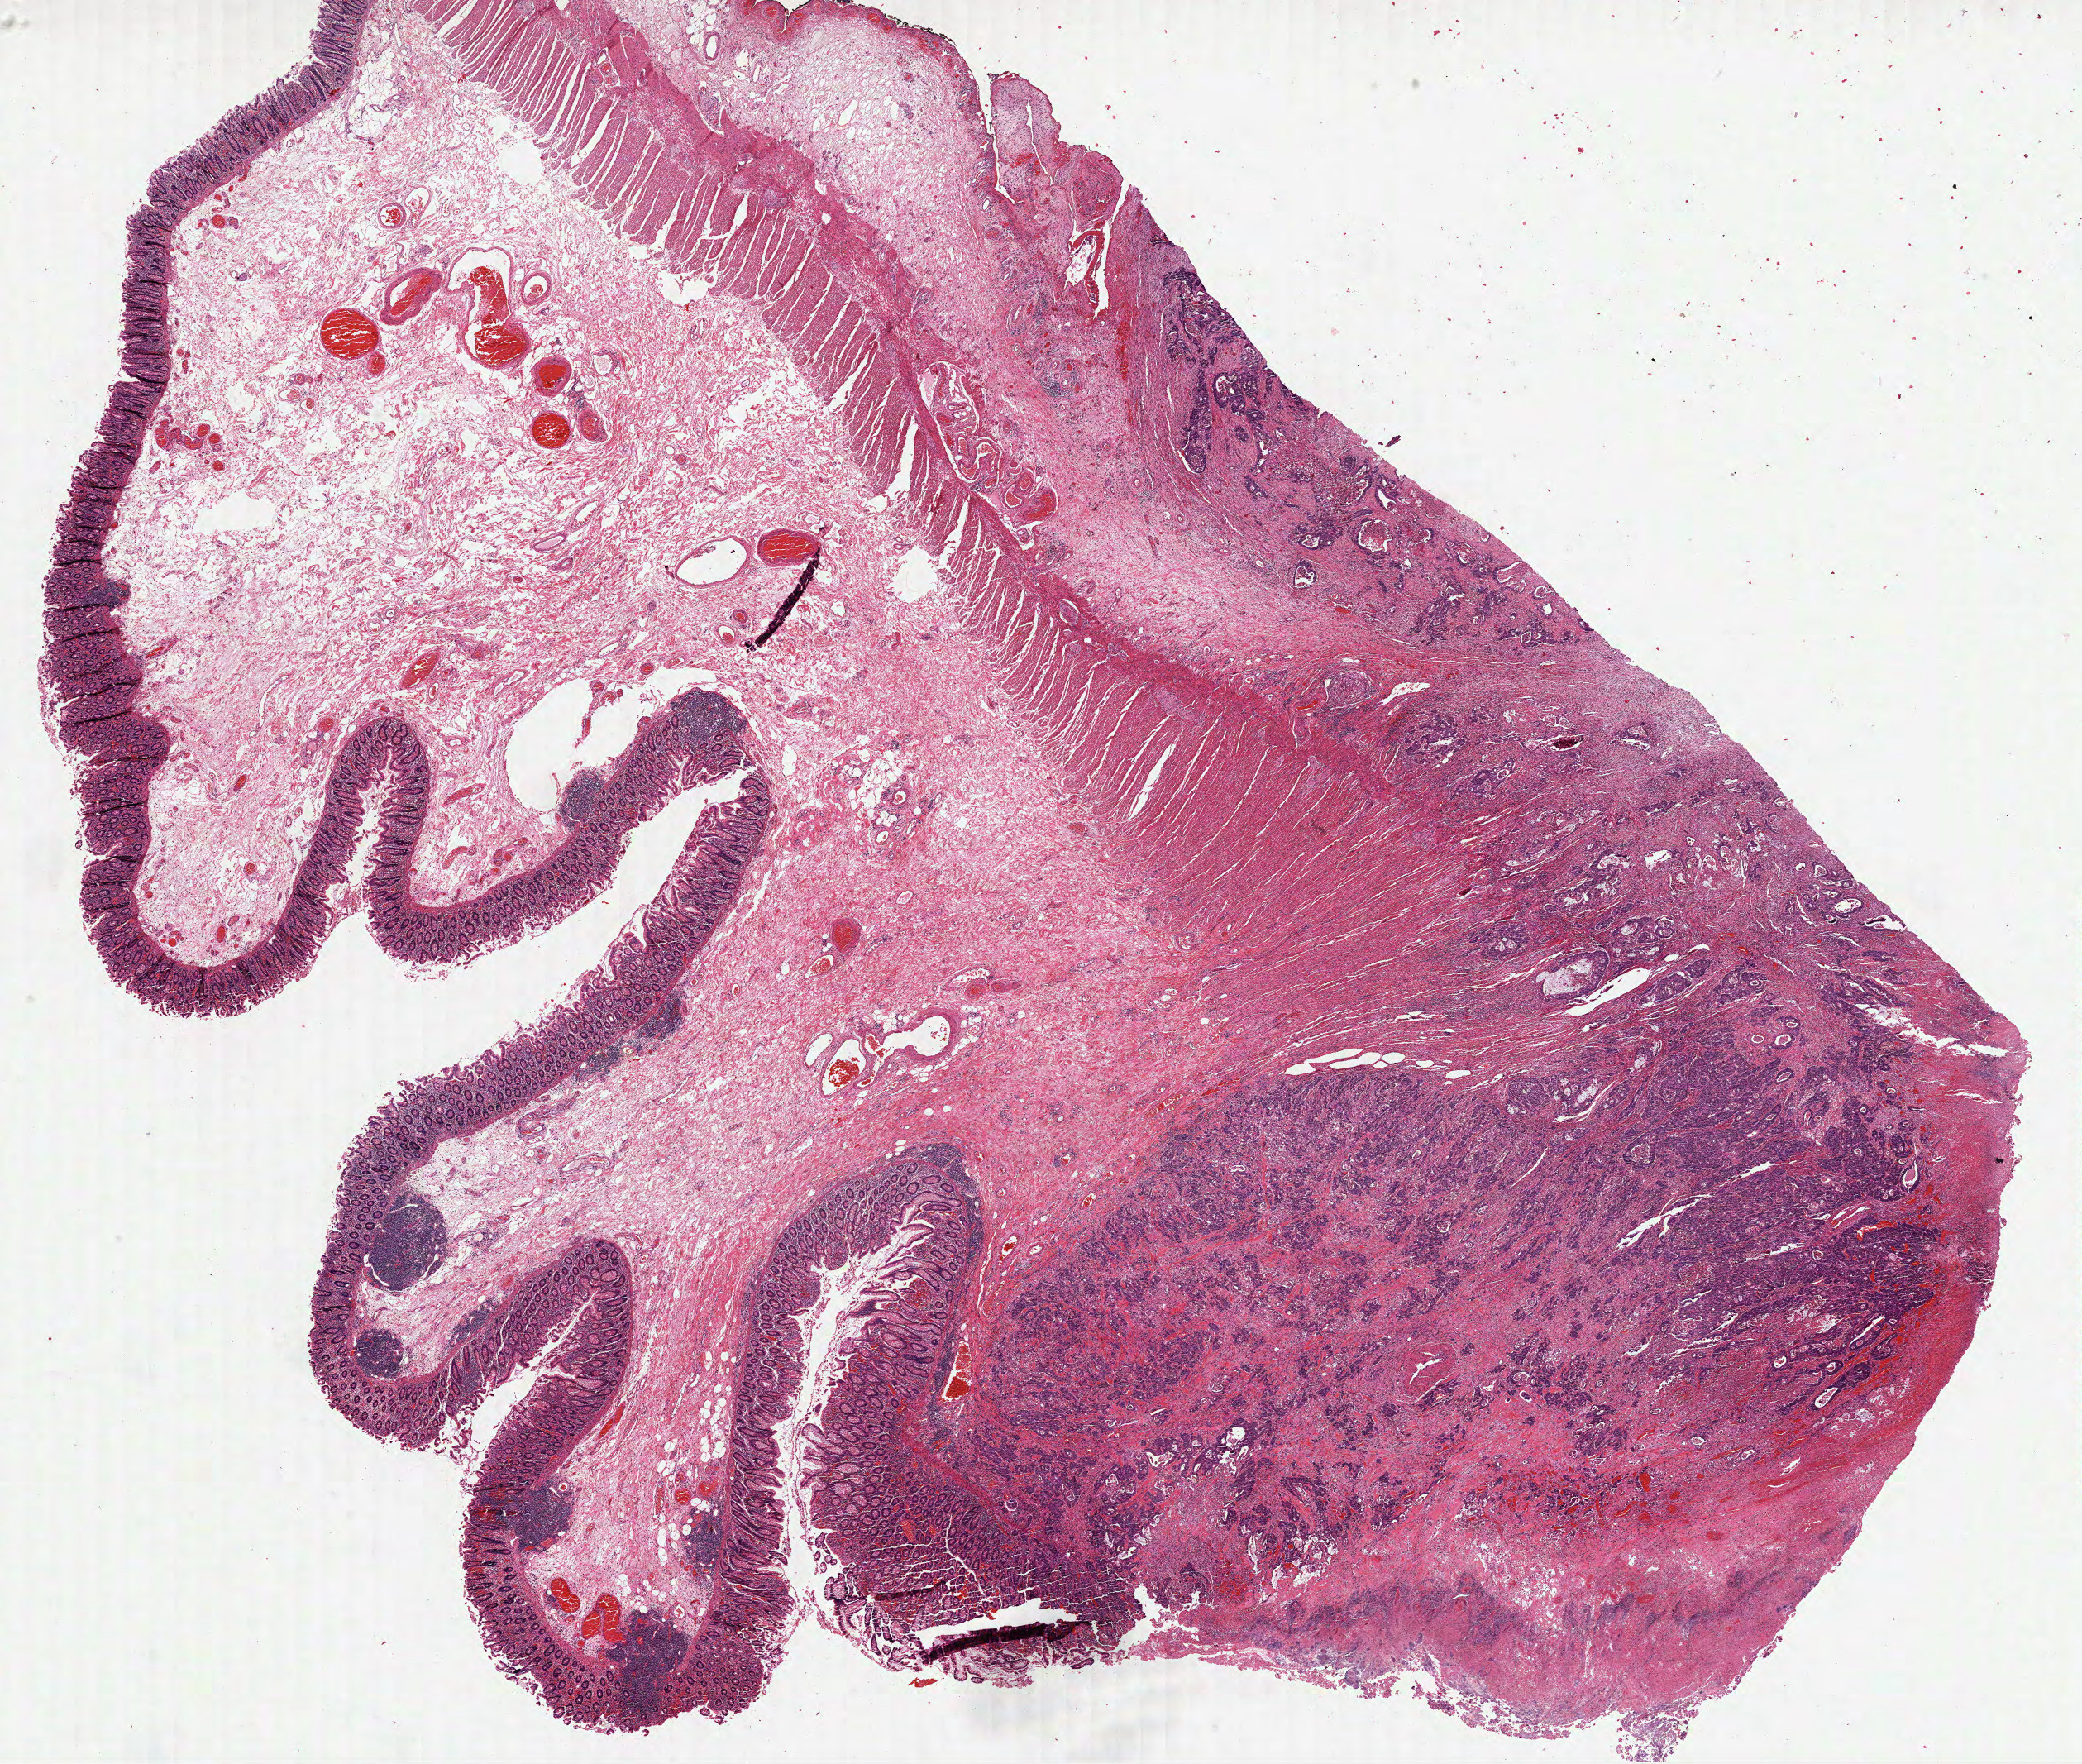
Digitized H&E tissue section (whole slide), whole scanned area (about 20.3 x 17.2 mm, from a 40x scan) shown as a low-resolution overview, FFPE section, colon, primary tumour sample. Patient: female, age at initial diagnosis 82 years.
Histologic diagnosis: Adenocarcinoma, NOS (cecum). AJCC pathologic stage: IV. Lymph nodes positive (case pathology): 13 of 23 examined.